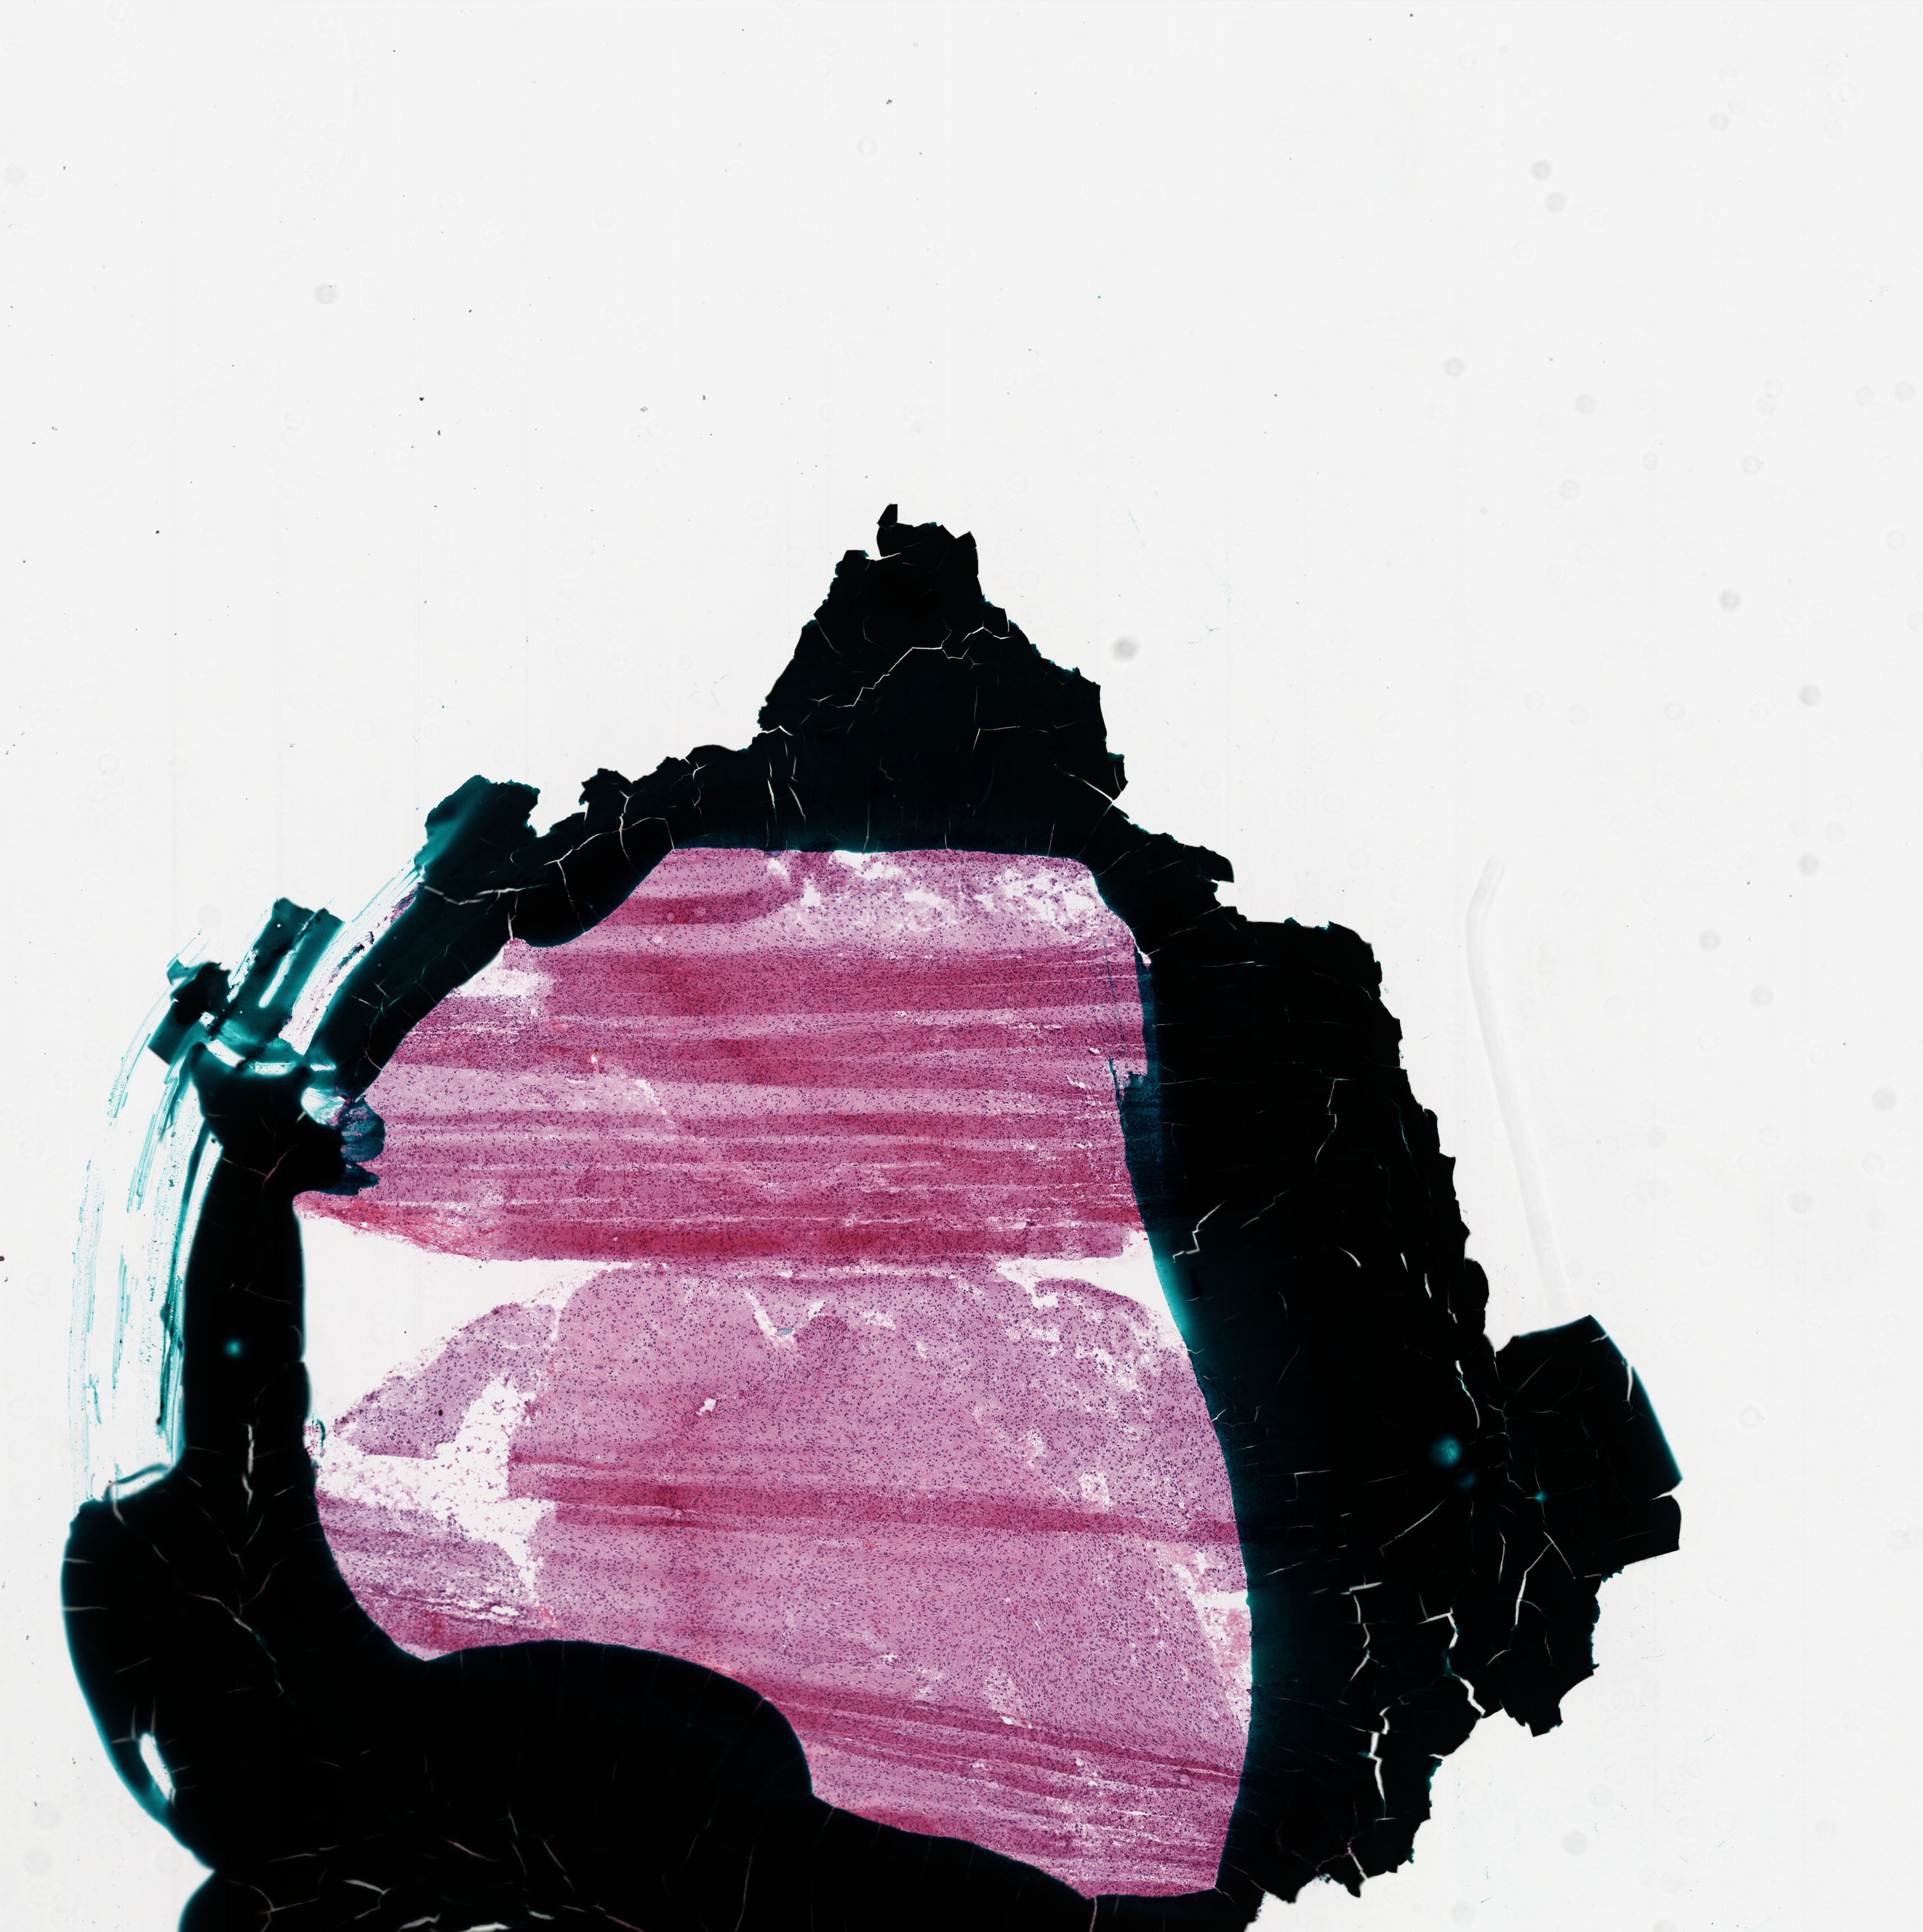
Digitized H&E tissue section (whole slide) — shown as a low-resolution overview of the whole scanned area (about 7.0 x 7.0 mm), frozen section, brain, primary tumour sample. Patient: female, age at initial diagnosis 63 years. Pathologist review of this section (percent, as recorded): tumour cells 95%, tumour nuclei 100%, normal cells 0%, stromal cells 0%, necrosis 5%.
- pathologic diagnosis: Glioblastoma